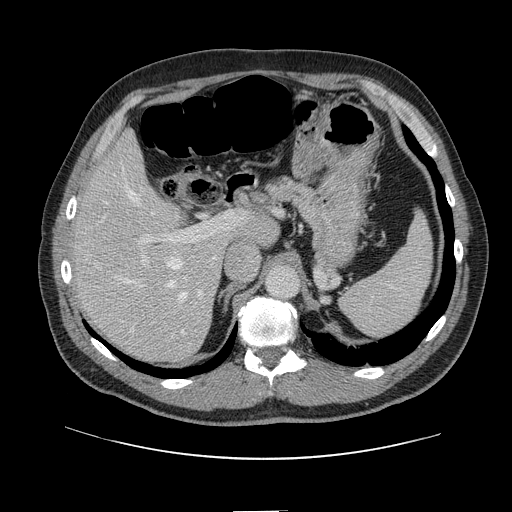
Contrast-enhanced abdominal CT, one axial slice. Position 89 of 161 along the scan axis. 120 kVp. Intravenous contrast given. Soft-tissue window (W 400 / L 40 HU). 2.5 mm slice thickness. 512 × 512 image matrix, field of view 412 × 412 mm. Male patient, age 66 years. Case-level facts recorded for this patient, not image findings: diagnosis: colorectal cancer liver metastases, imaged before liver resection; multiple liver metastases: no; largest metastasis: 3.5 cm; disease in both lobes: no.
Structures marked on this image (expert manual segmentation):
- hepatic veins: box from (x=105, y=172) to (x=188, y=332) px
- liver: (x=76, y=137)–(x=275, y=361)
- planned liver remnant (the part of the liver to remain after resection): (x=75, y=137)–(x=276, y=305)
- portal vein (with intrahepatic branches): (x=137, y=212)–(x=242, y=308)